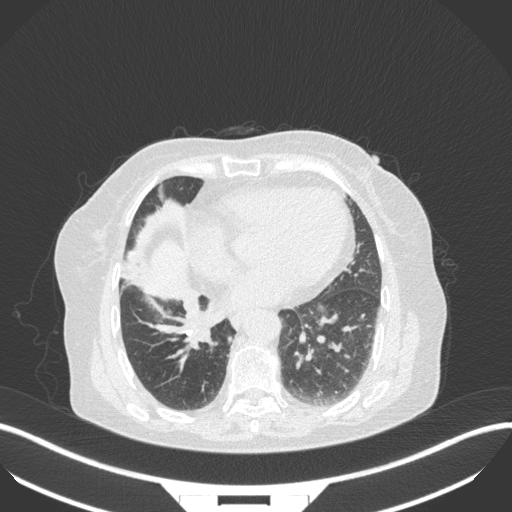
Chest CT, one axial slice. Slice 117 of 329 in the series (ordered by position). Lung window (W 1500 / L -600 HU). 1 mm slice thickness. 512 × 512 image matrix, field of view 400 × 400 mm. Female patient, age 75 years. Case-level facts recorded for this patient, not image findings: clinical TNM (as recorded): T1b N0 M1a; histopathological grade: G1.
Structures marked on this image (bounding box drawn by a radiologist):
- lung tumour (recorded histology: squamous cell carcinoma): box from (x=183, y=307) to (x=221, y=349) px